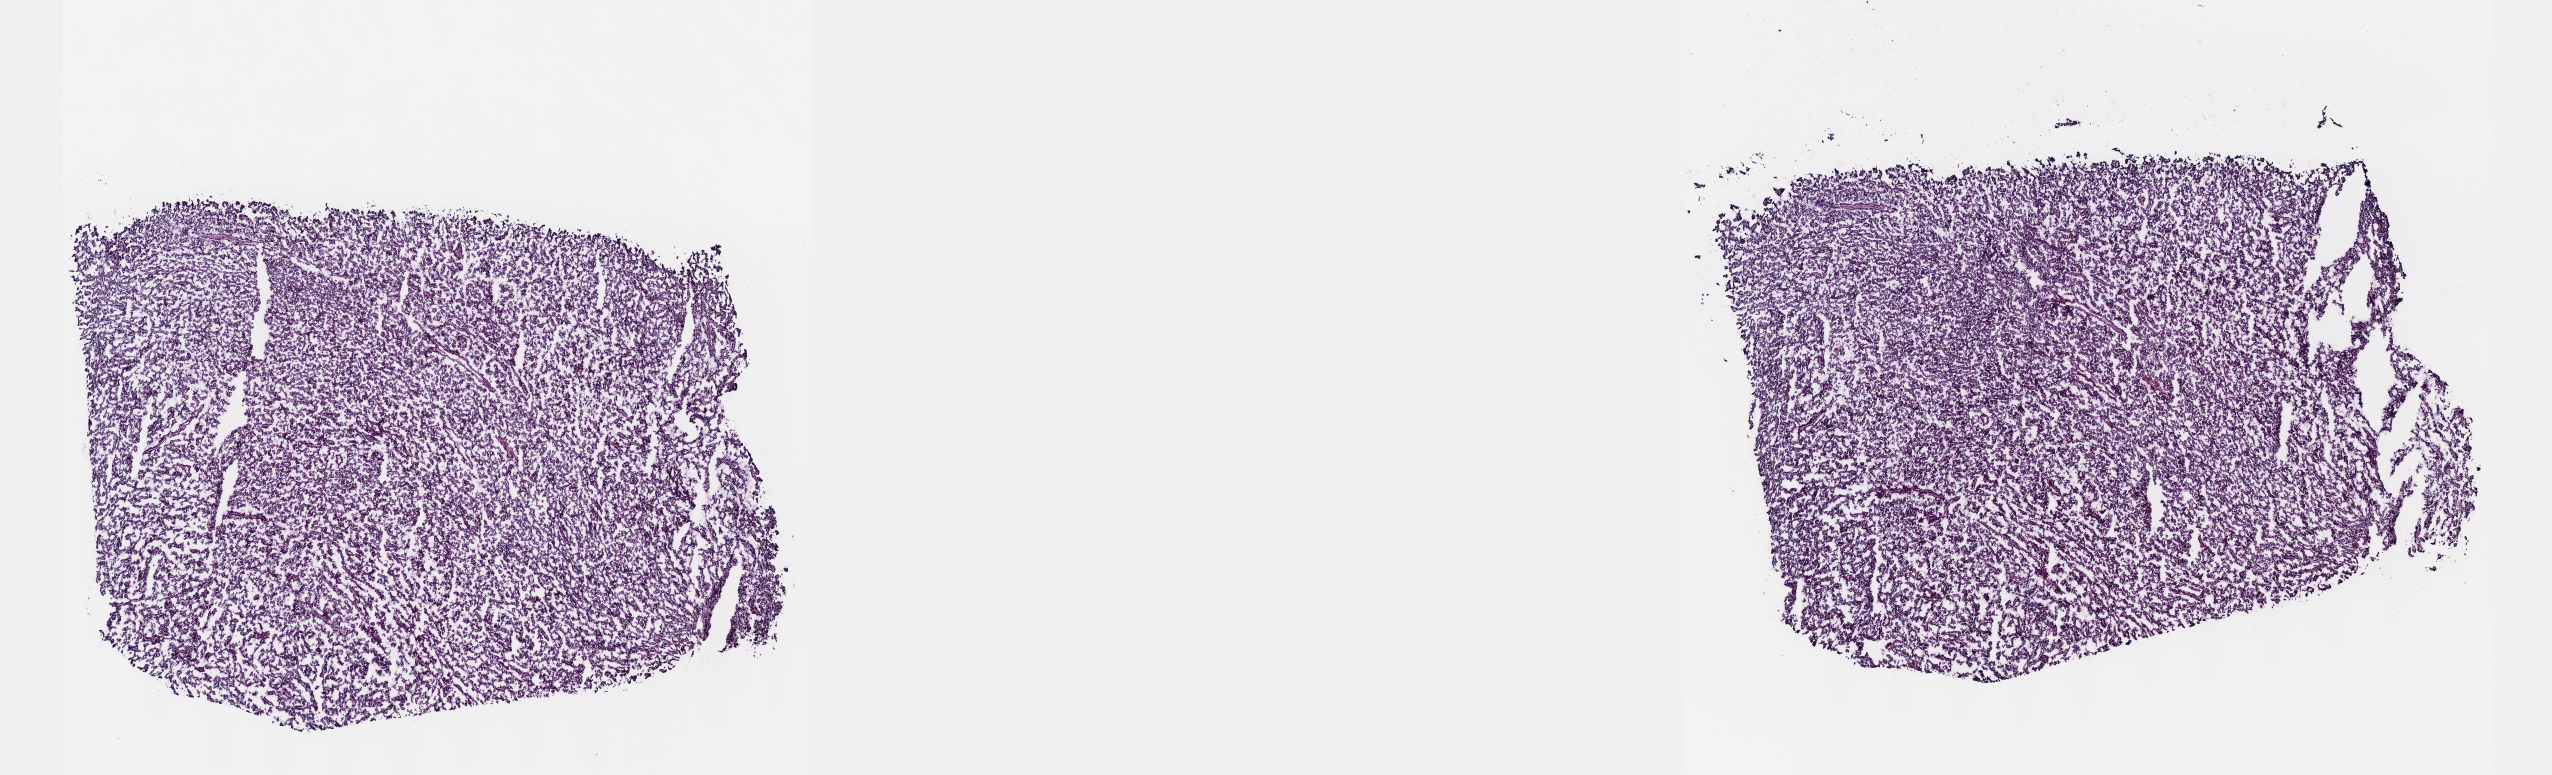
H&E whole-slide image — low-resolution overview of the scanned area, about 20.6 x 6.3 mm (slide scanned at 40x), frozen section from the top of the tissue portion, sample: primary tumour, kidney. Patient: male, age at initial diagnosis 70 years.
Pathologic diagnosis: Papillary adenocarcinoma, NOS.